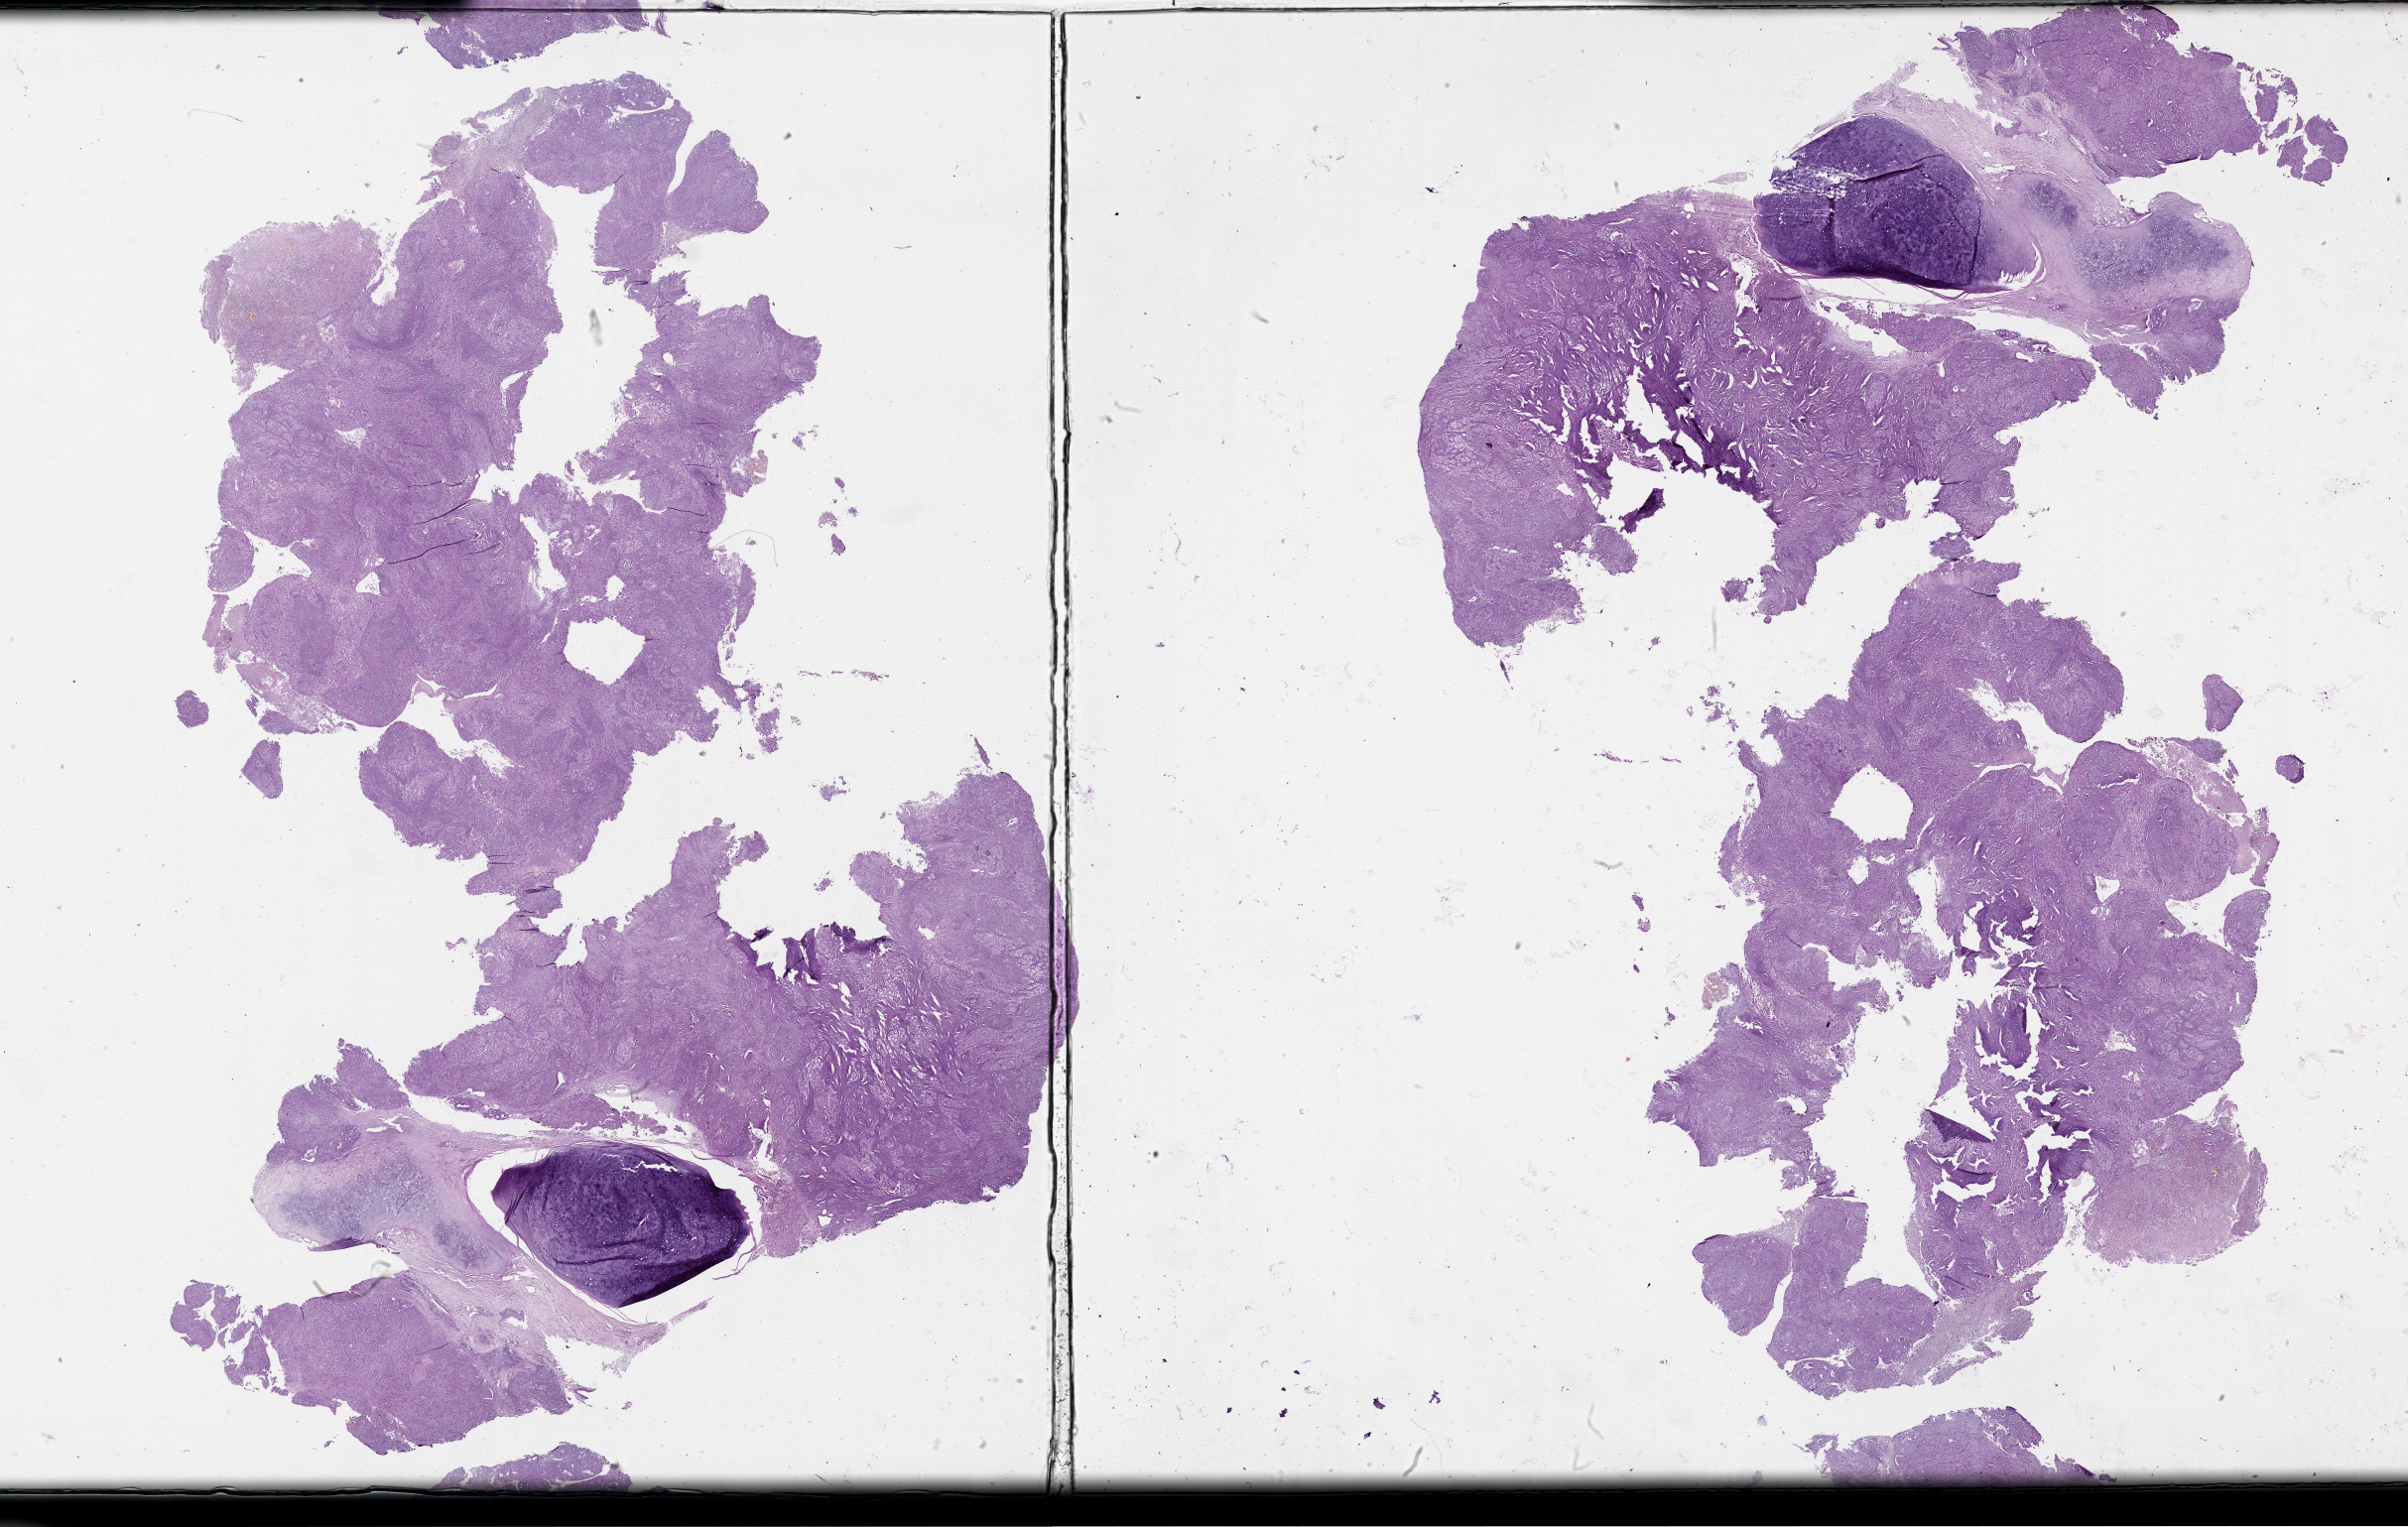
Whole-slide histology image, H&E-stained — whole scanned area (about 39.1 x 24.8 mm, from a 20x scan) shown as a low-resolution overview; tumour tissue sample, sampled site: larynx. 55-year-old male patient. Histologic grade: G2 (moderately differentiated). Slide review estimates, as recorded: tumour nuclei 80%, necrosis 12%.
- AJCC pathologic stage: III
- diagnosis: Squamous cell carcinoma, NOS
- primary tumour site (as recorded): larynx